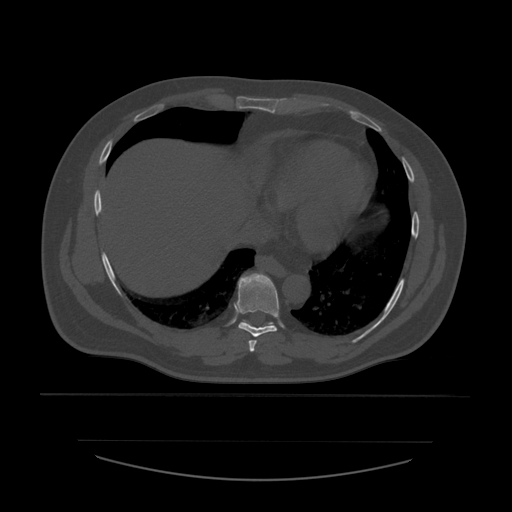
CT including the spine, one axial slice; position 334 of 532 along the scan axis; reconstruction kernel STANDARD; bone window (W 1800 / L 400 HU); 1.25 mm slice thickness; 512 × 512 image matrix. Patient age 44 years. Case-level facts recorded for this patient, not image findings: primary cancer: soft tissue sarcoma.
Annotated regions visible in this slice (semi-automatic segmentation, software-assisted and operator-edited):
- T7 vertebra: bounding box (x1, y1, x2, y2) in pixels: (249, 340, 257, 353)
- T8 vertebra: (234, 274, 279, 337)
- T9 vertebra: (243, 320, 274, 326)